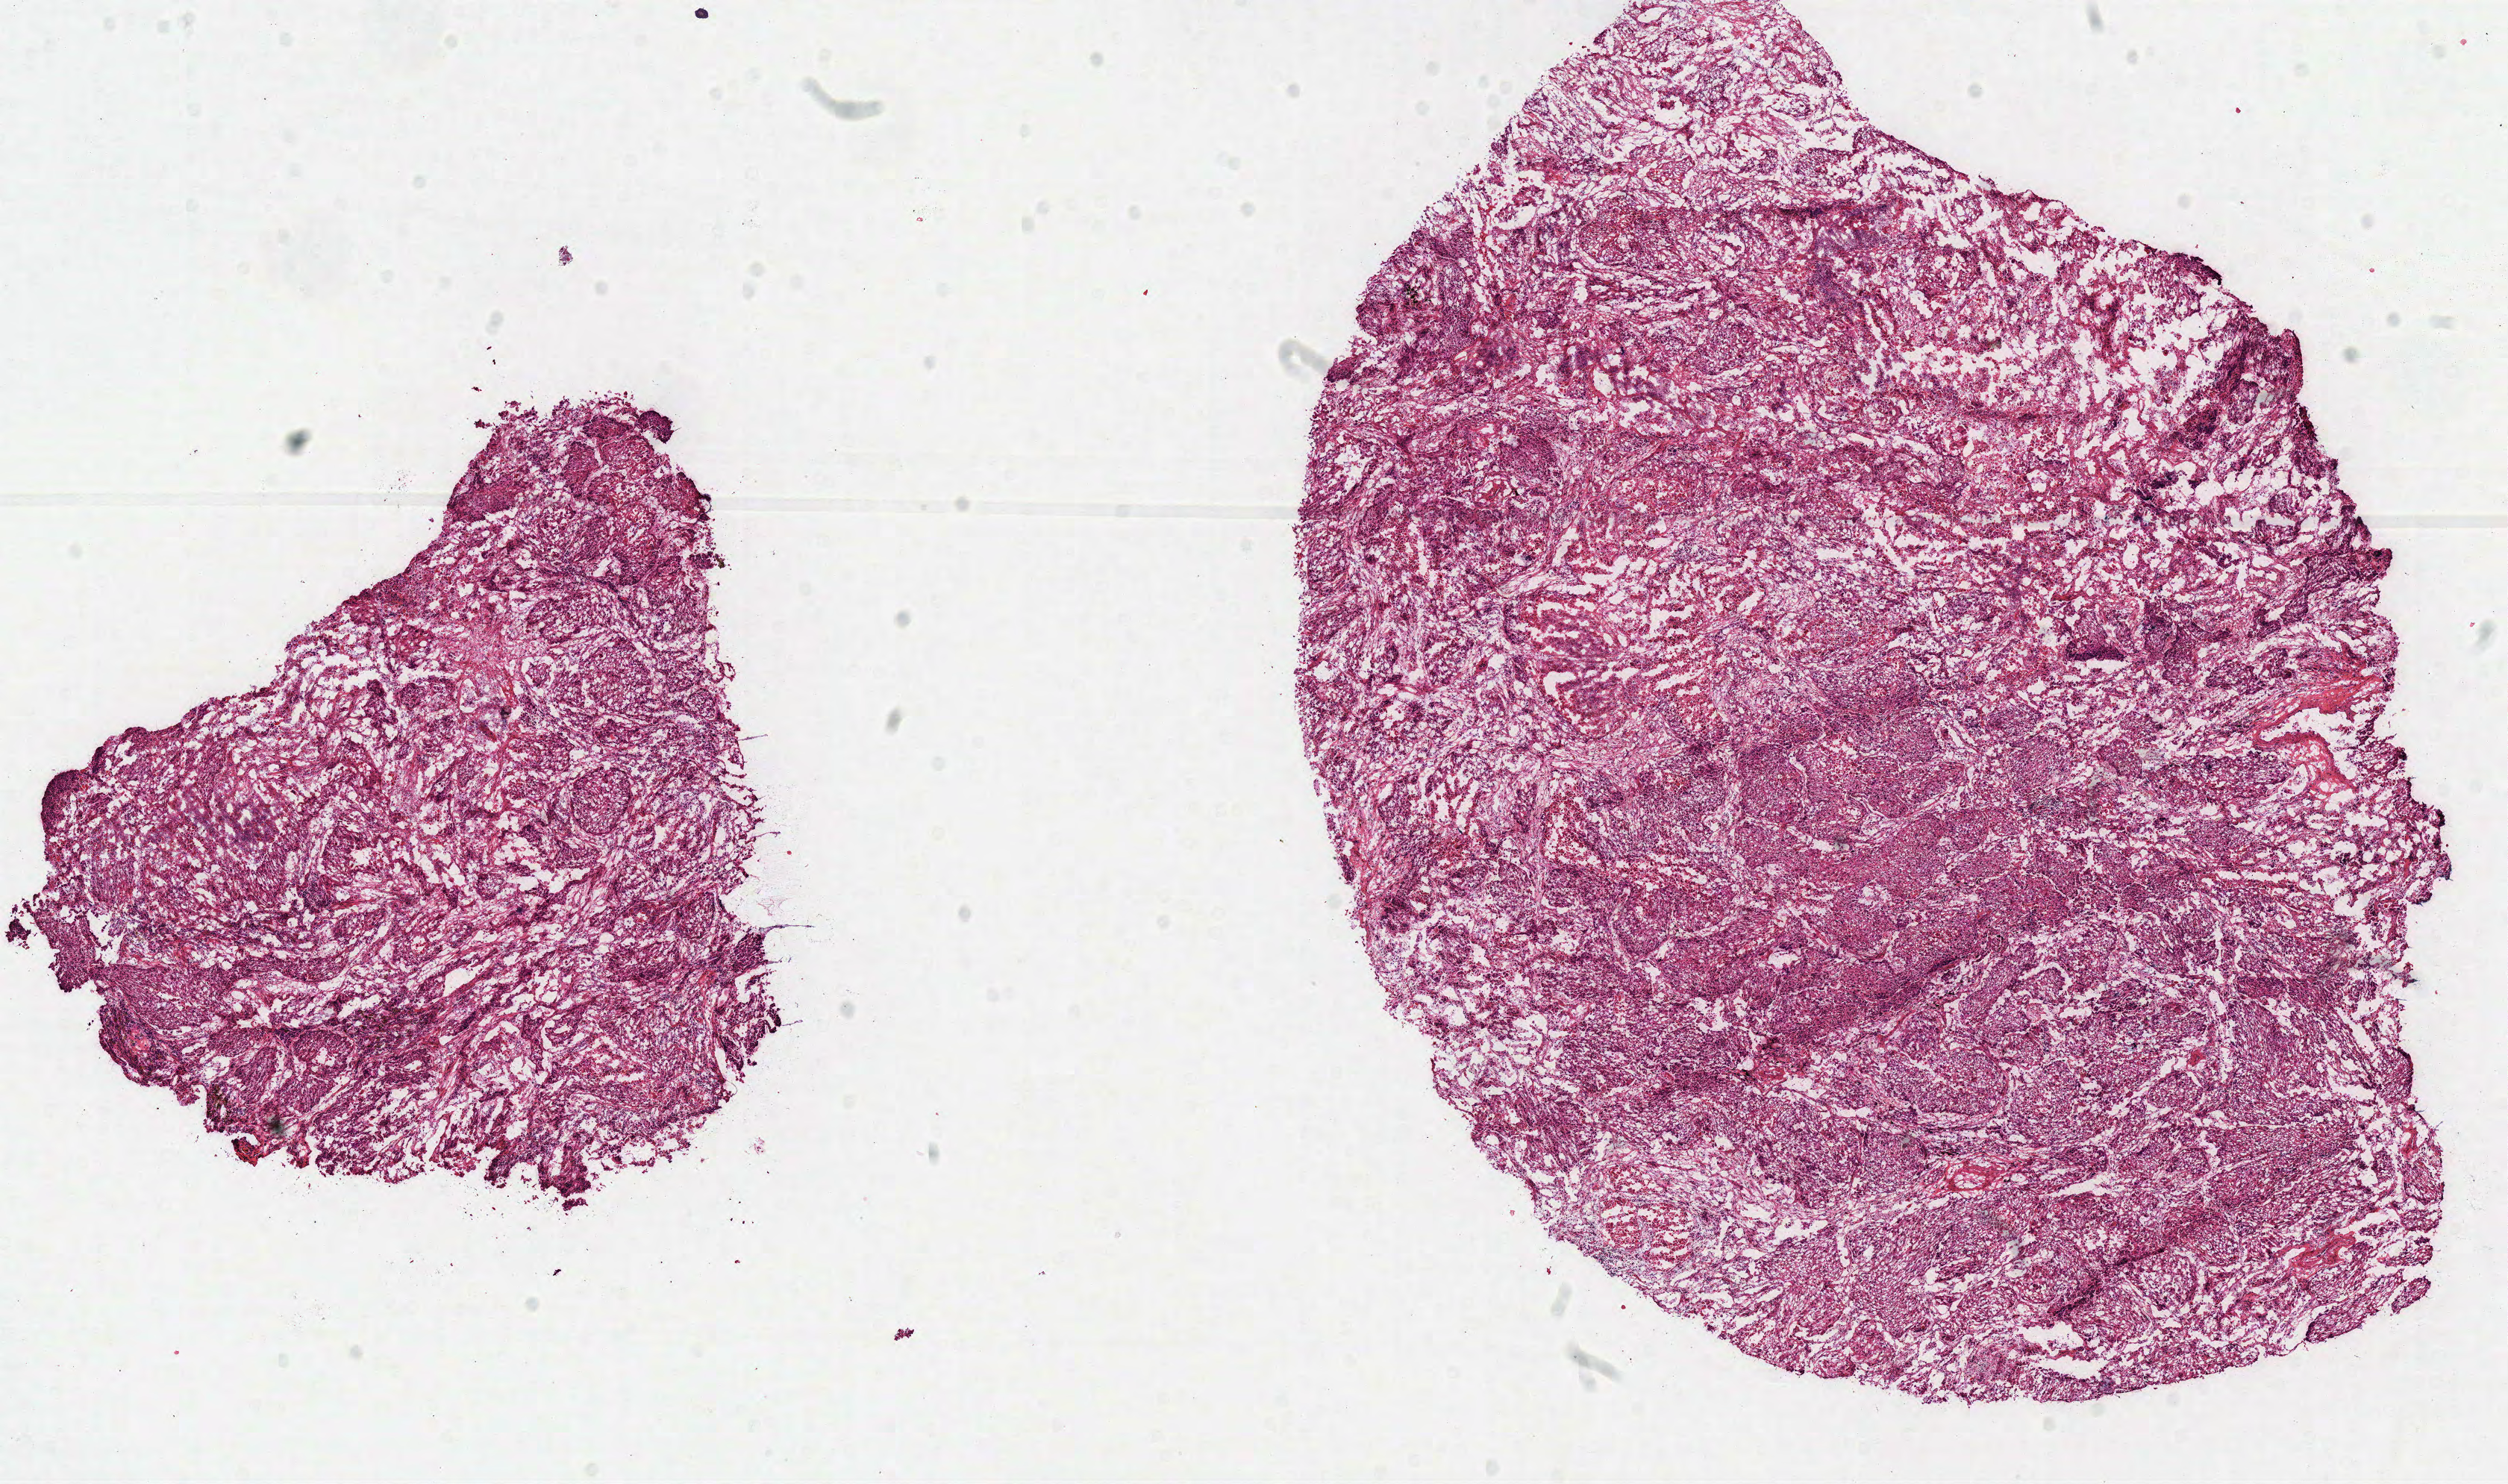
H&E-stained whole-slide image — a low-resolution overview of the entire scanned area, about 13.2 x 7.8 mm, frozen section from the top of the tissue portion, sample: primary tumour, lung. Male patient; age at initial diagnosis 73 years. Slide review estimates, as recorded: tumour cells 93%, tumour nuclei 80%, normal cells 0%, stromal cells 0%, necrosis 7%. Infiltration values recorded for this section: lymphocyte infiltration 5%, monocyte infiltration 1%, neutrophil infiltration 2%.
AJCC pathologic stage: IB. Histologic diagnosis: Squamous cell carcinoma, NOS.